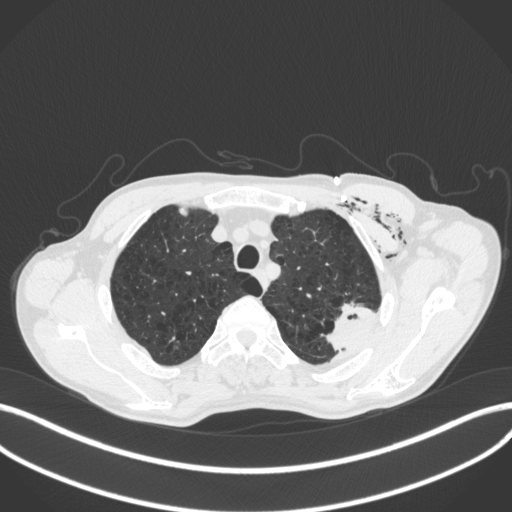
Chest CT, one axial slice. Slice 341 of 416 in the series (ordered by position). 120 kVp. Lung window (W 1500 / L -600 HU). 1 mm slice thickness. 512 × 512 image matrix, field of view 400 × 400 mm. Male patient, age 58 years. Case-level facts recorded for this patient, not image findings: clinical TNM (as recorded): T3 N0 M0.
Annotated regions visible in this slice (rectangle marked by the reading radiologist):
- lung tumour (recorded histology: adenocarcinoma): bounding box [x1, y1, x2, y2] px = [317, 297, 377, 360]